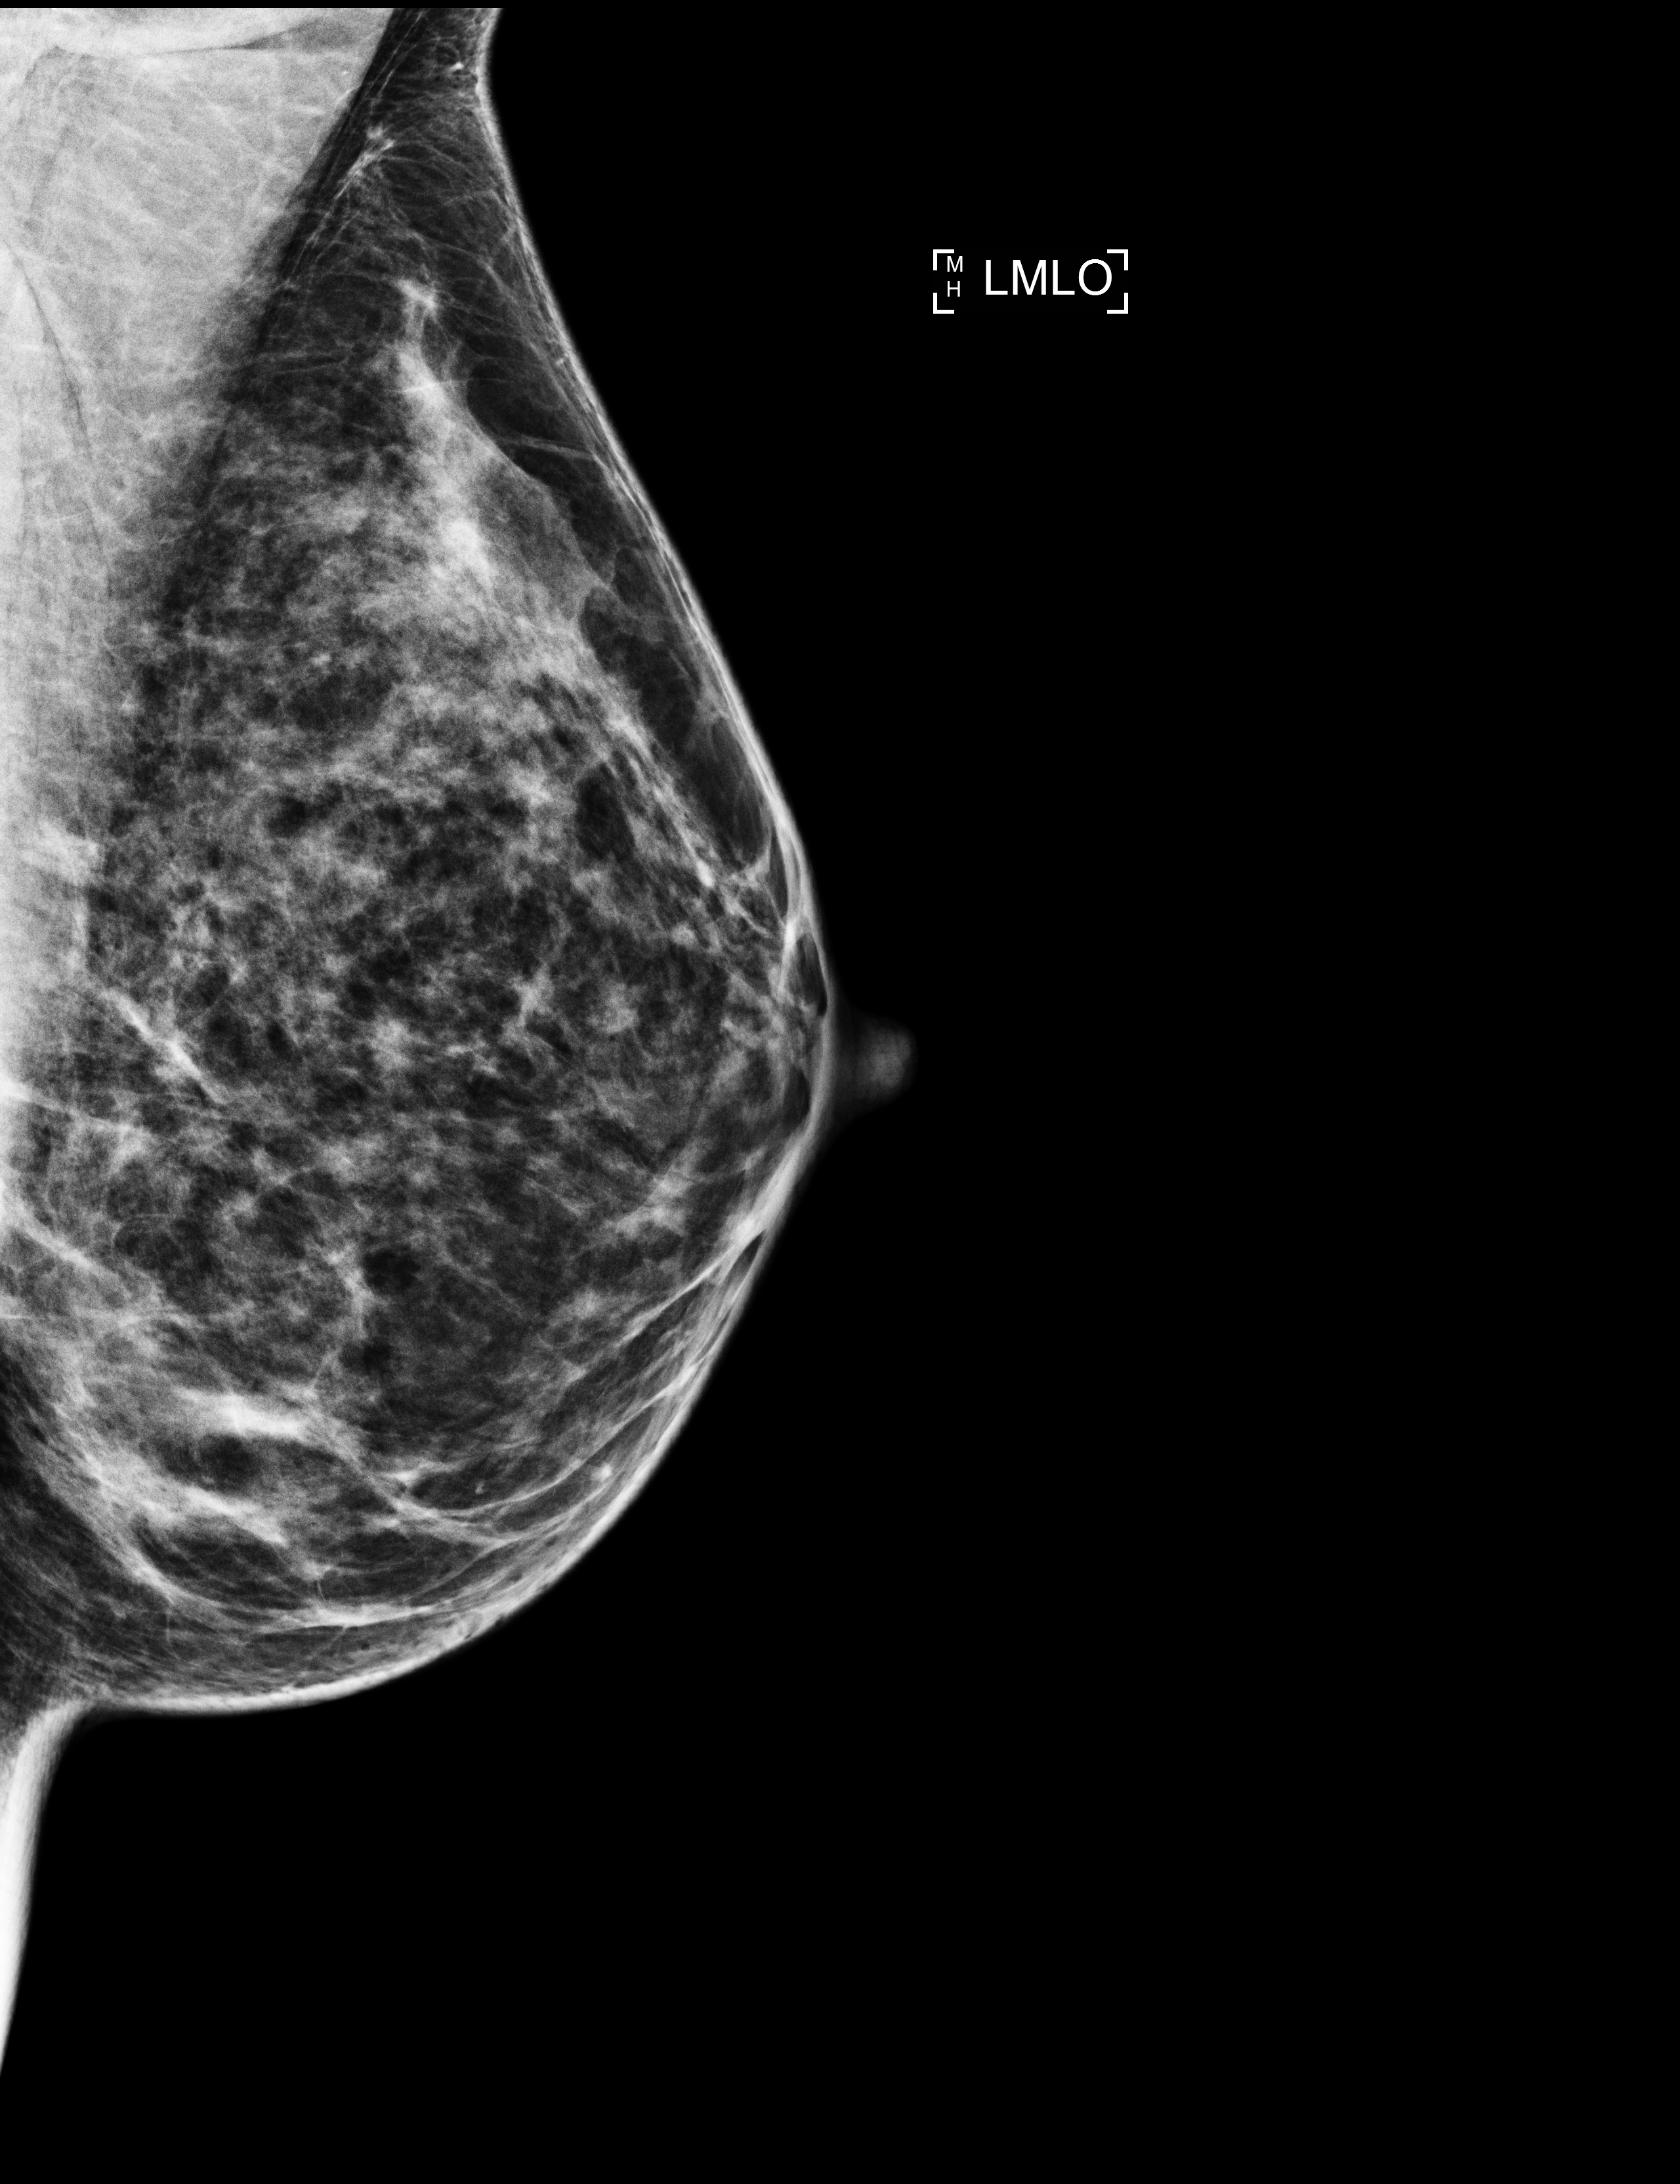
Annual screening mammography examination. Patient aged 42 years (female).
Image type: full-field digital mammogram. Breast: left. Projection: MLO view.